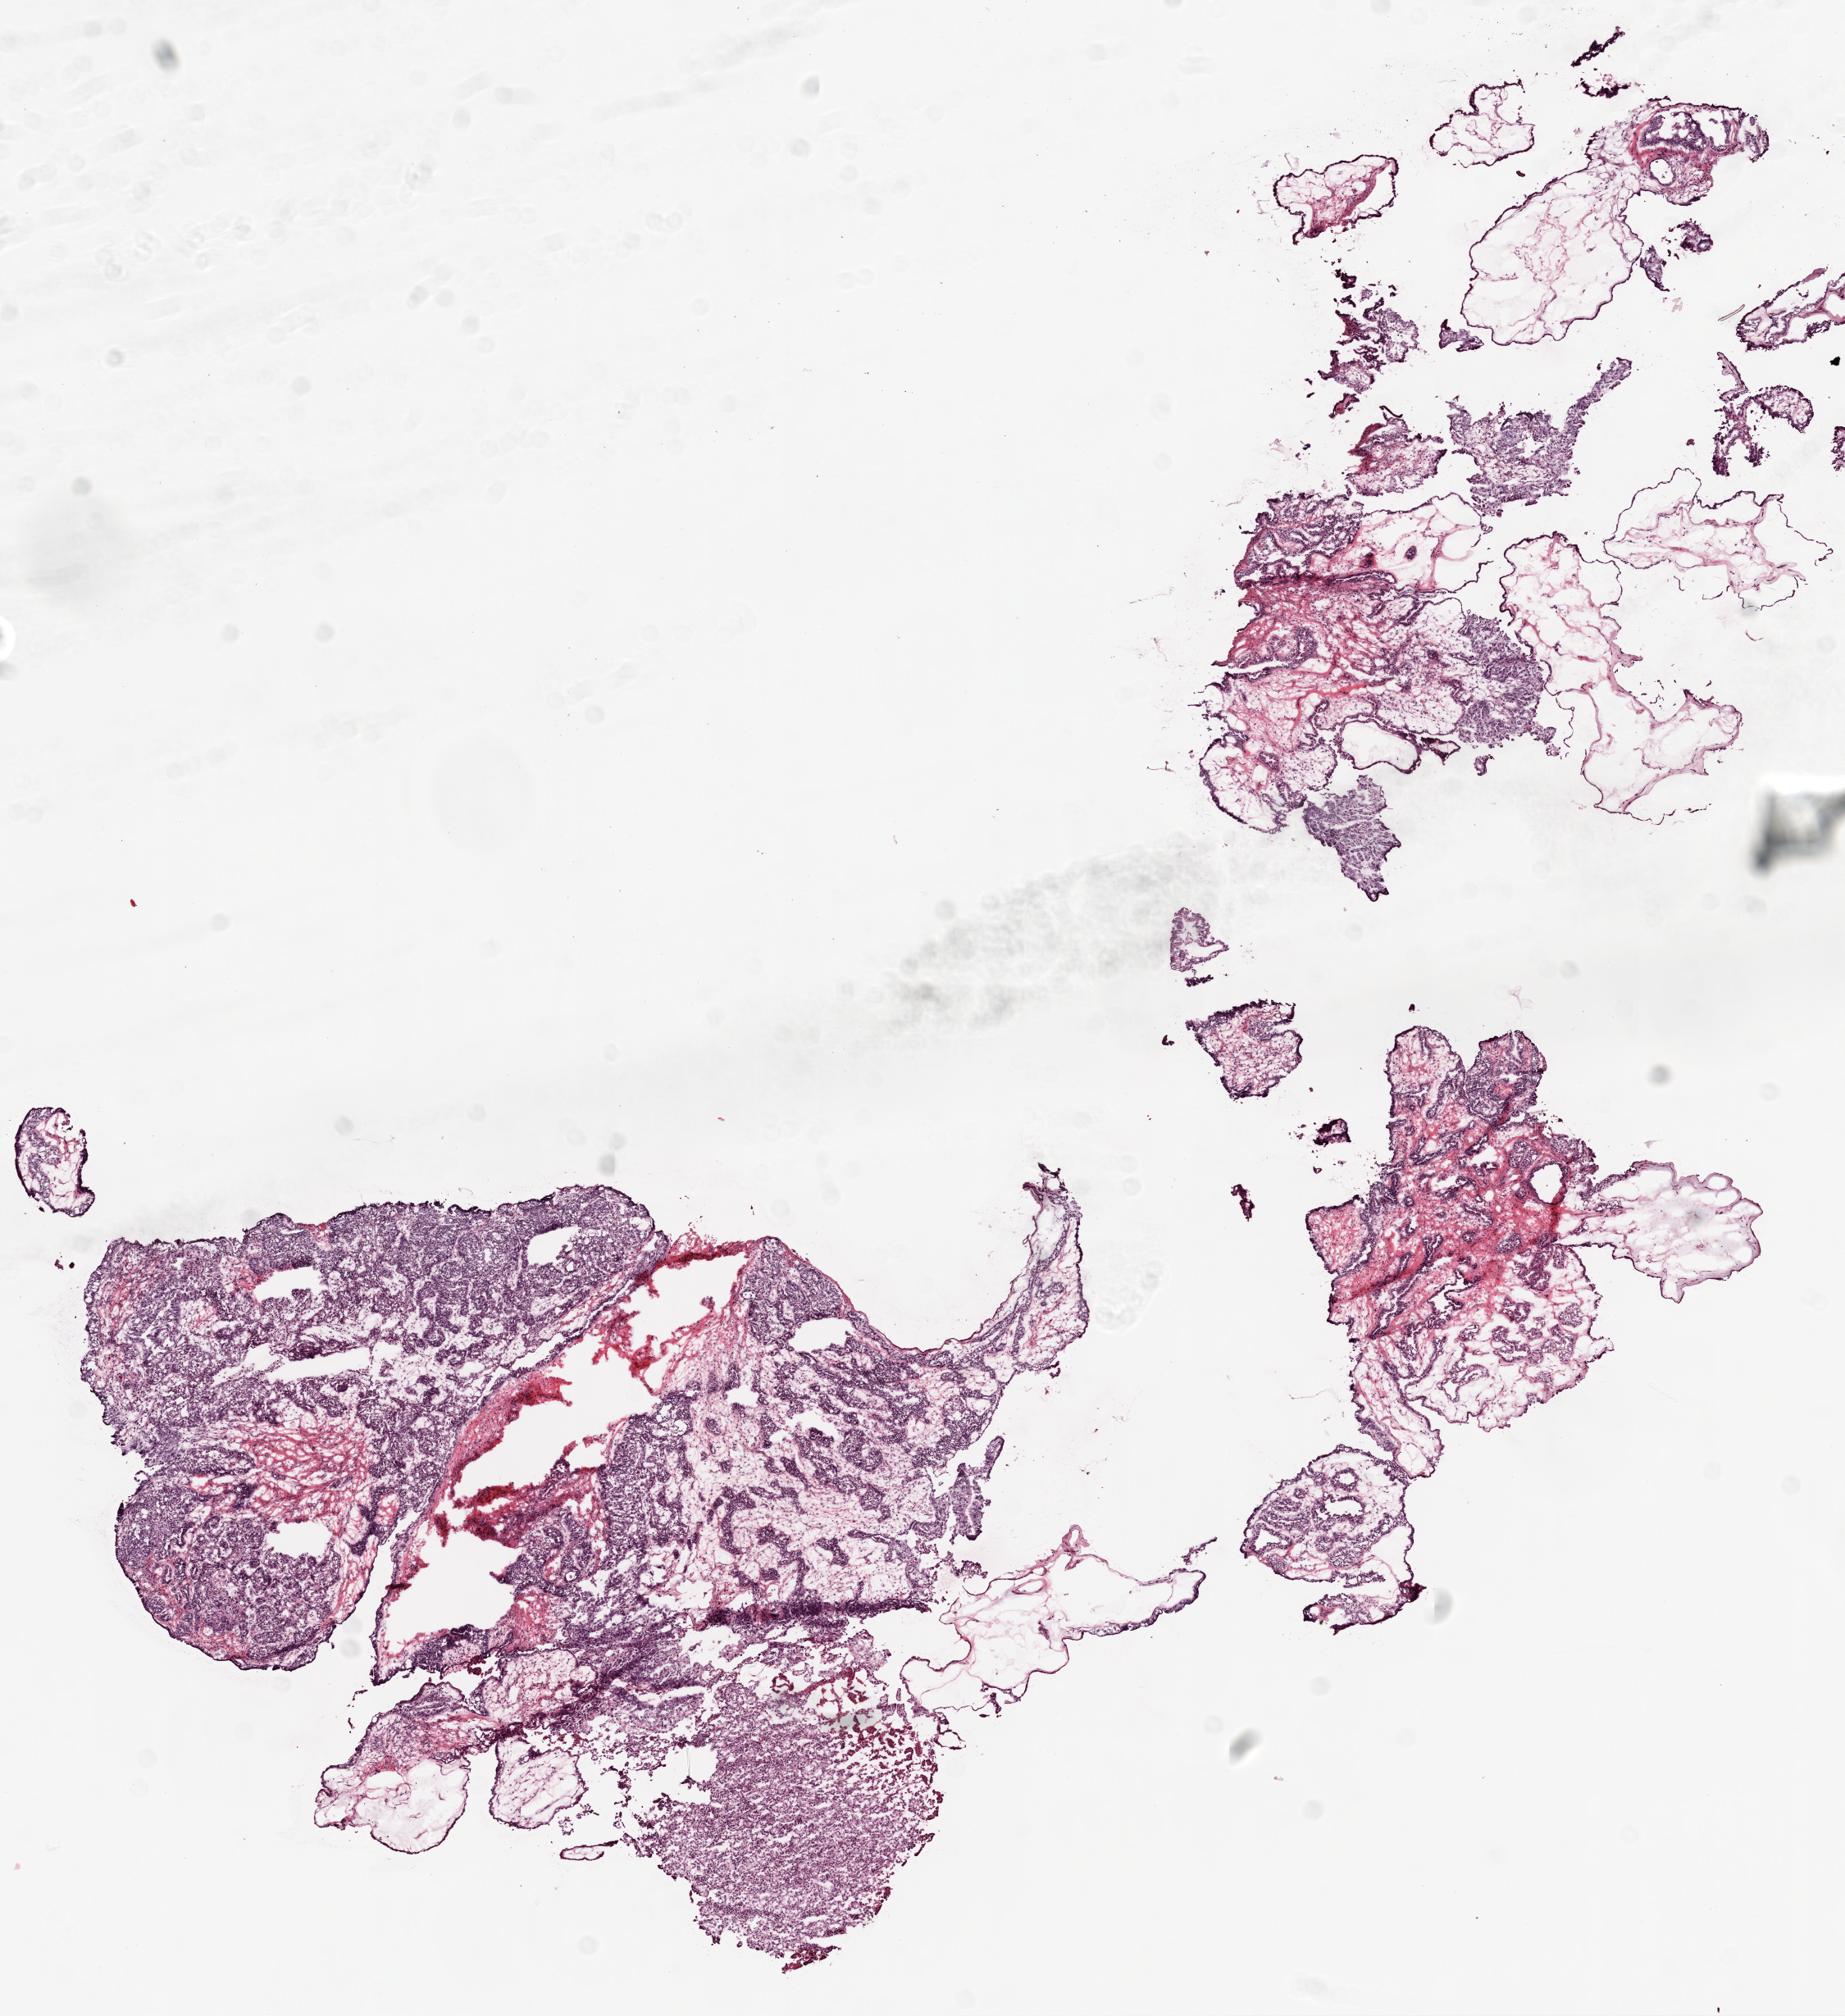
H&E whole-slide image, whole scanned area (about 9.0 x 9.9 mm, from a 20x scan) shown as a low-resolution overview; frozen section from the top of the tissue portion; ovary, primary tumour sample. Female patient; age at initial diagnosis 76 years. Histologic grade: G2 (moderately differentiated). Composition of this section per pathologist review: tumour cells 80%, tumour nuclei 90%, normal cells 0%, stromal cells 20%, necrosis 0%.
• FIGO stage: IIIC
• histologic diagnosis: Serous cystadenocarcinoma, NOS